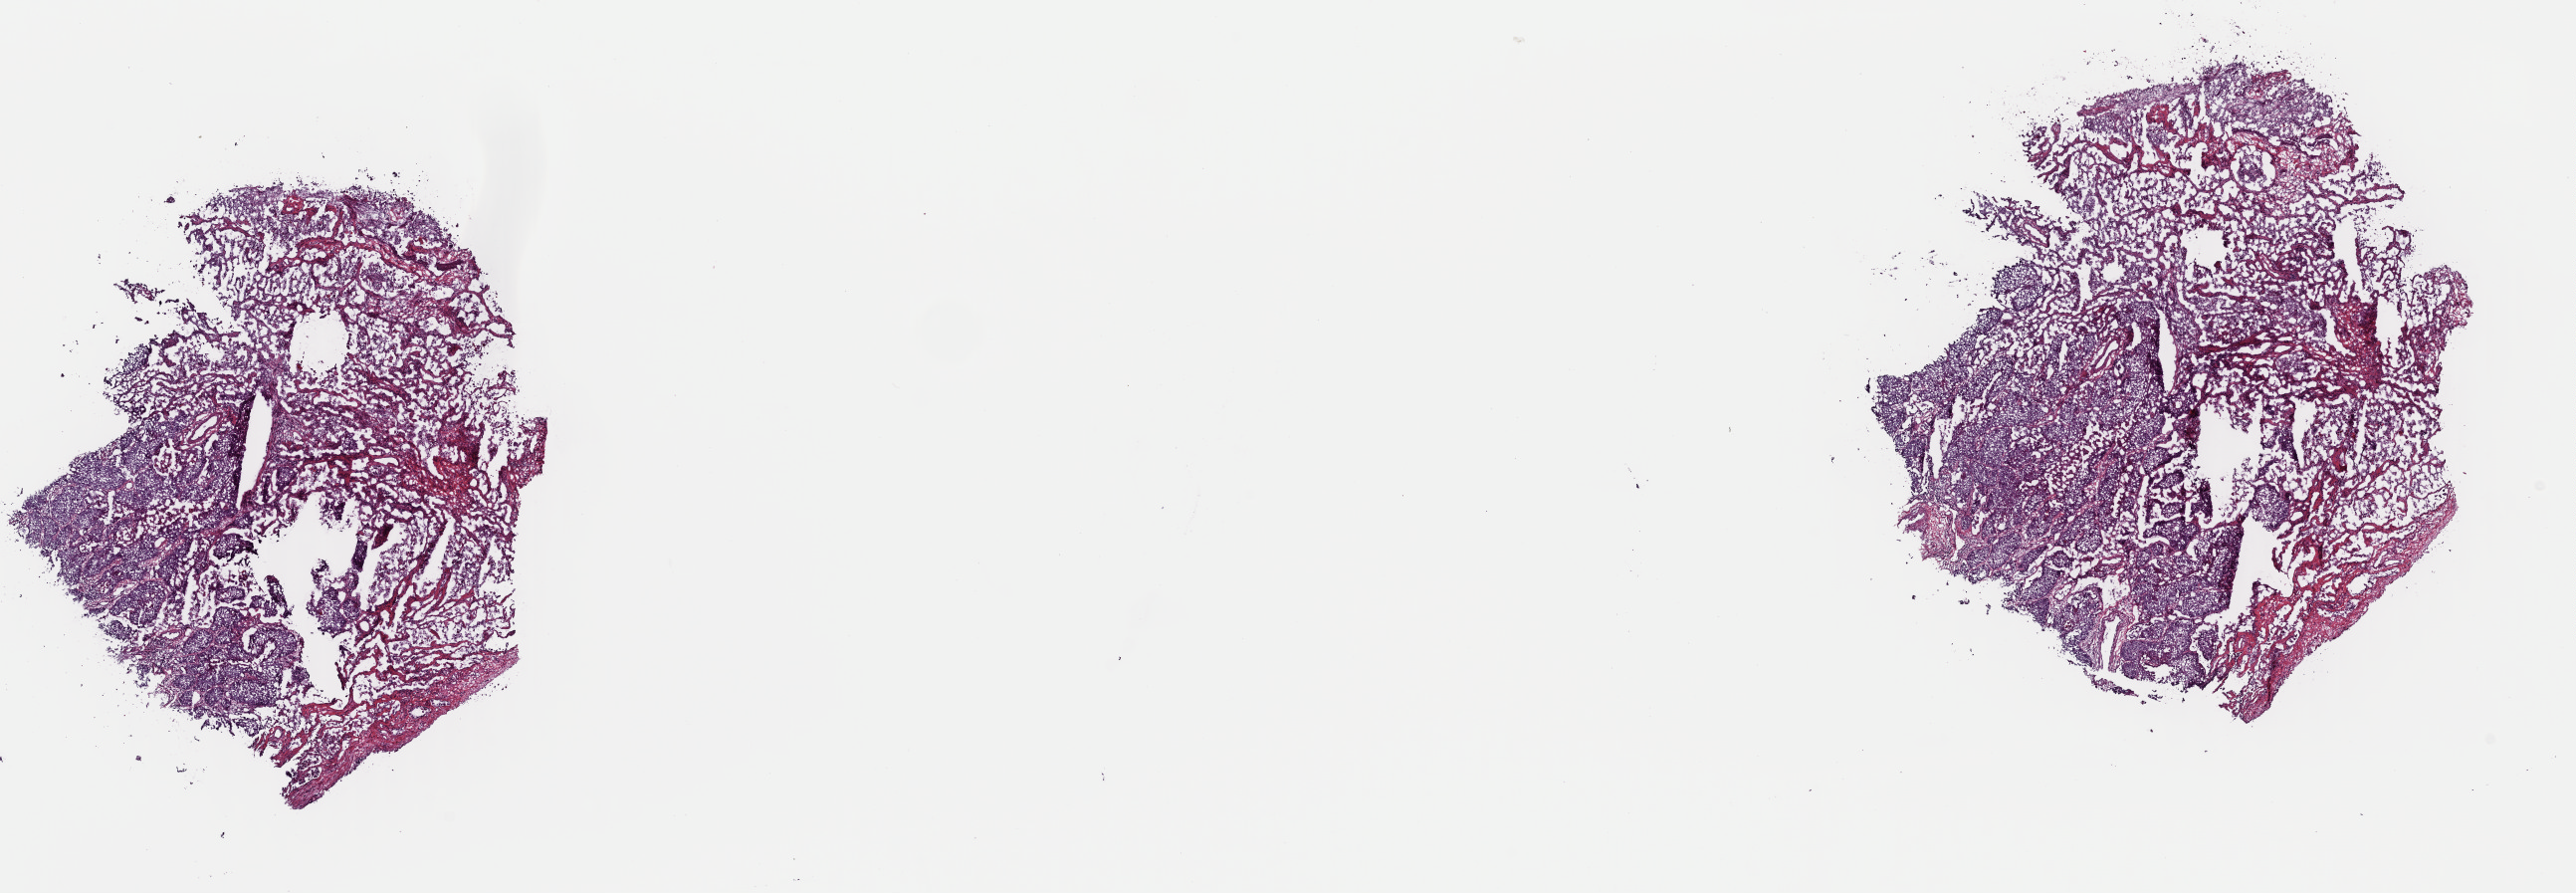
Digitized H&E tissue section (whole slide) — a low-resolution overview of the entire scanned area, about 20.4 x 7.1 mm; frozen section from the top of the tissue portion; lung, primary tumour sample. Male patient; age at initial diagnosis 63 years. Composition of this section per pathologist review: tumour cells 50%, tumour nuclei 65%, normal cells 30%, stromal cells 10%, necrosis 10%. Infiltration values recorded for this section: lymphocyte infiltration 0%, monocyte infiltration 0%, neutrophil infiltration 0%.
• laterality: right
• TNM: T2 N0 MX
• histologic diagnosis: Squamous cell carcinoma, NOS (middle lobe, lung)
• AJCC pathologic stage: I (6th edition)